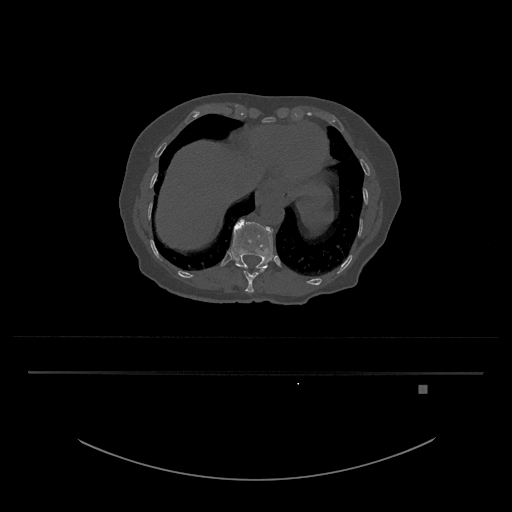
CT including the spine, one axial slice. Position 635 of 797 along the scan axis. Reconstruction kernel Br40s/3. 120 kVp. Bone window (W 1800 / L 400 HU). 0.5 mm slice thickness. 512 × 512 image matrix. Female patient, age 57 years. Case-level facts recorded for this patient, not image findings: primary cancer: cervical.
Annotated regions visible in this slice (semi-automatic segmentation, software-assisted and operator-edited):
- T11 vertebra: bounding box [x1, y1, x2, y2] px = [240, 266, 266, 293]
- T12 vertebra: [231, 219, 273, 270]